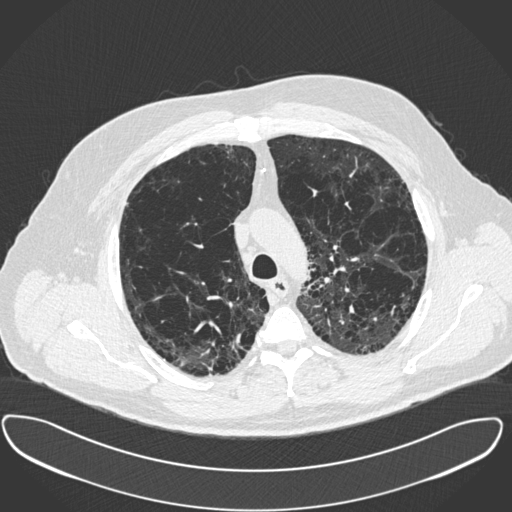
Low-dose screening chest CT, one axial slice. Position 289 of 385 along the scan axis. 120 kVp. Lung window (W 1500 / L -600 HU). 512 × 512 image matrix, field of view 408 × 408 mm.
Structures marked on this image (manually delineated by an expert):
- lesion 1 (tumor, upper lobe of right lung): box from (x=236, y=332) to (x=242, y=345) px